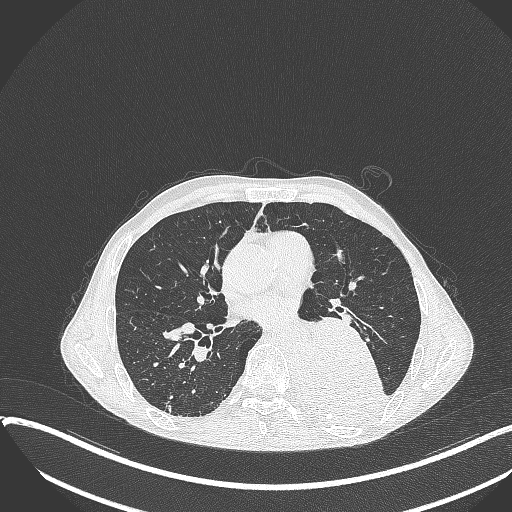
Chest CT, one axial slice. Slice 186 of 401 in the series (ordered by position). 120 kVp. Lung window (W 1500 / L -600 HU). 1 mm slice thickness. 512 × 512 image matrix. Male patient, age 57 years. Case-level facts recorded for this patient, not image findings: clinical TNM (as recorded): T4 N0 M0.
Outlined on this slice (bounding box drawn by a radiologist):
- lung tumour (recorded histology: squamous cell carcinoma): box from (x=294, y=313) to (x=390, y=426) px